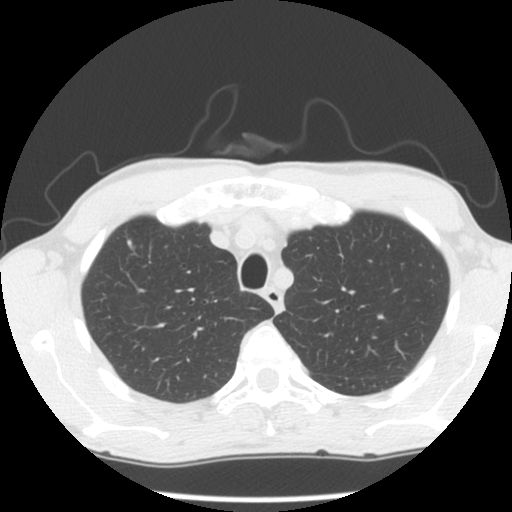
Chest CT (low-dose screening protocol), one axial image; second screening round (one year after baseline); lung window (W 1500 / L -600 HU); slice 113 of 142 in the series. Male participant, aged 56 years at enrolment. Current smoker at enrolment.
- Expert-annotated lung lesion, bounding box <107,229,156,273> (left, top, right, bottom; pixels).
- No non-calcified nodule or mass ≥4 mm was recorded by the screening reader at this exam.
- Official screen result: negative screen, minor abnormalities not suspicious for lung cancer.
- Lung cancer was diagnosed 345 days after this screen: small cell carcinoma, NOS, right upper lobe, stage IV (AJCC 6th edition).